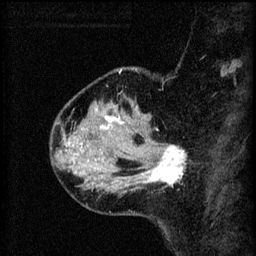
Breast MRI (dynamic contrast-enhanced), one sagittal slice. Position 17 of 60 along the scan axis. 3 images stored at this slice position (order not interpretable as contrast timing). 1.5 T. TE 4.2 ms, TR 8.2 ms. 2 mm slice thickness. 256 × 256 image matrix, field of view 180 × 180 mm. Patient: female, 37 years.
Outlined on this slice (semi-automatically segmented with operator editing):
- analysis volume of interest (the breast-tissue region the enhancement analysis was run in; not a lesion): bounding box (x1, y1, x2, y2) in pixels: (124, 138, 186, 193)
- tumour enhancement mask (voxels above the 70 % enhancement threshold inside the analysis volume of interest): (131, 142, 185, 185)